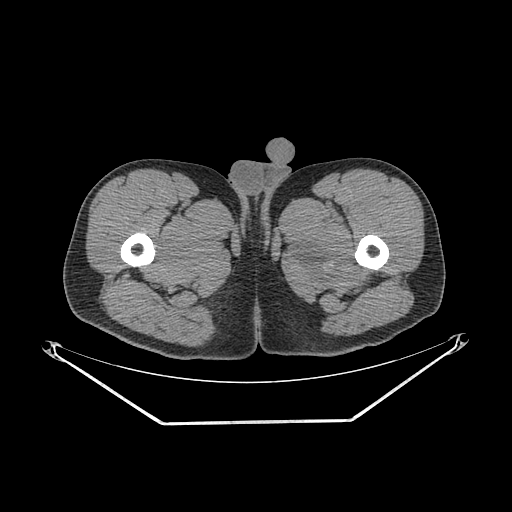
CT of an extremity soft-tissue mass (from a PET/CT study), one axial slice; slice 262 of 267 in the series (ordered by position); reconstruction kernel SOFT; 140 kVp; soft-tissue window (W 400 / L 40 HU); 512 × 512 image matrix. Male patient. Case-level facts recorded for this patient, not image findings: histological type: extraskeletal osteosarcoma; grade: high; site of the primary tumour: left adductur.
Annotated regions visible in this slice (expert contour drawn on MRI and transferred to this co-registered scan by the dataset authors):
- gross tumour volume (mass): box from (x=285, y=201) to (x=387, y=300) px